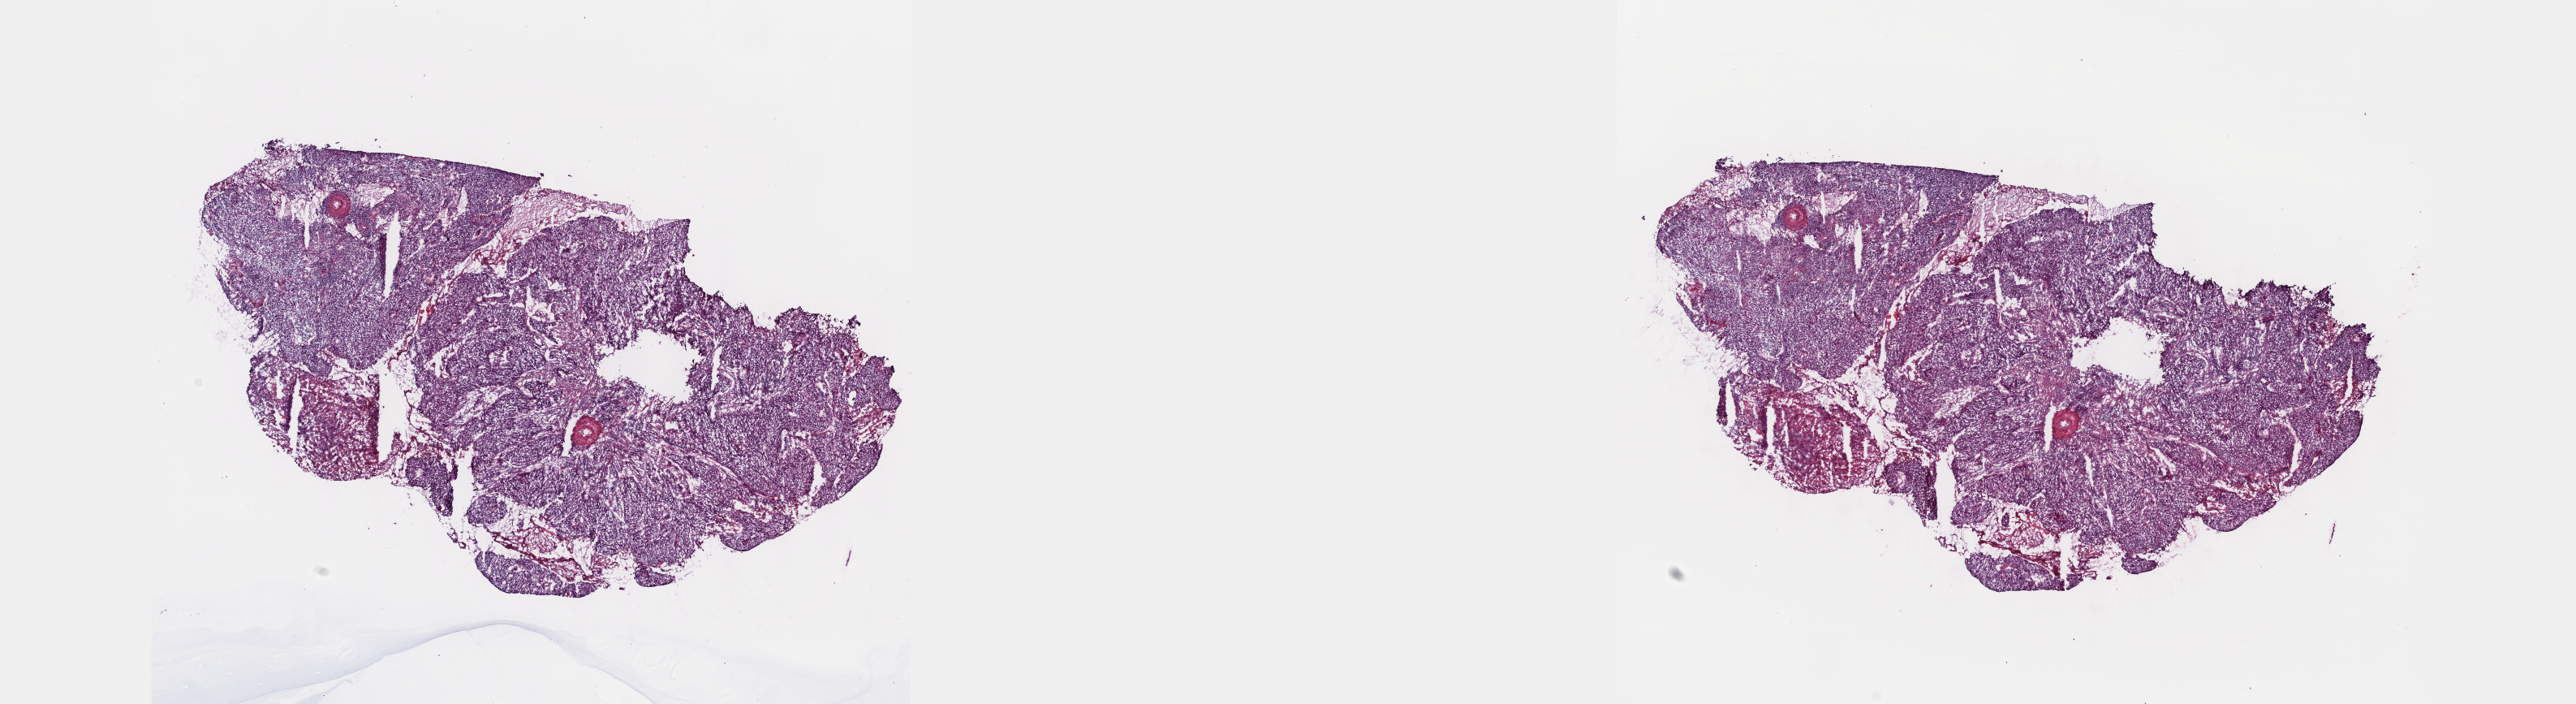
Digitized Hematoxylin and eosin (H&E) stained tissue section (whole slide), low-resolution overview of the scanned area, about 25.7 x 7.0 mm (slide scanned at 40x). Frozen section from the top of the tissue portion. Primary tumour sample from the cervix. Female, age 40 years at initial diagnosis. Histologic grade: G2 (moderately differentiated). Composition of this section per pathologist review: tumour cells 70%, tumour nuclei 70%, normal cells 0%, stromal cells 20%, necrosis 10%. Infiltration values recorded for this section: lymphocyte infiltration 40%, monocyte infiltration 20%, neutrophil infiltration 20%.
Diagnosis: Squamous cell carcinoma, NOS. FIGO stage: IIB.